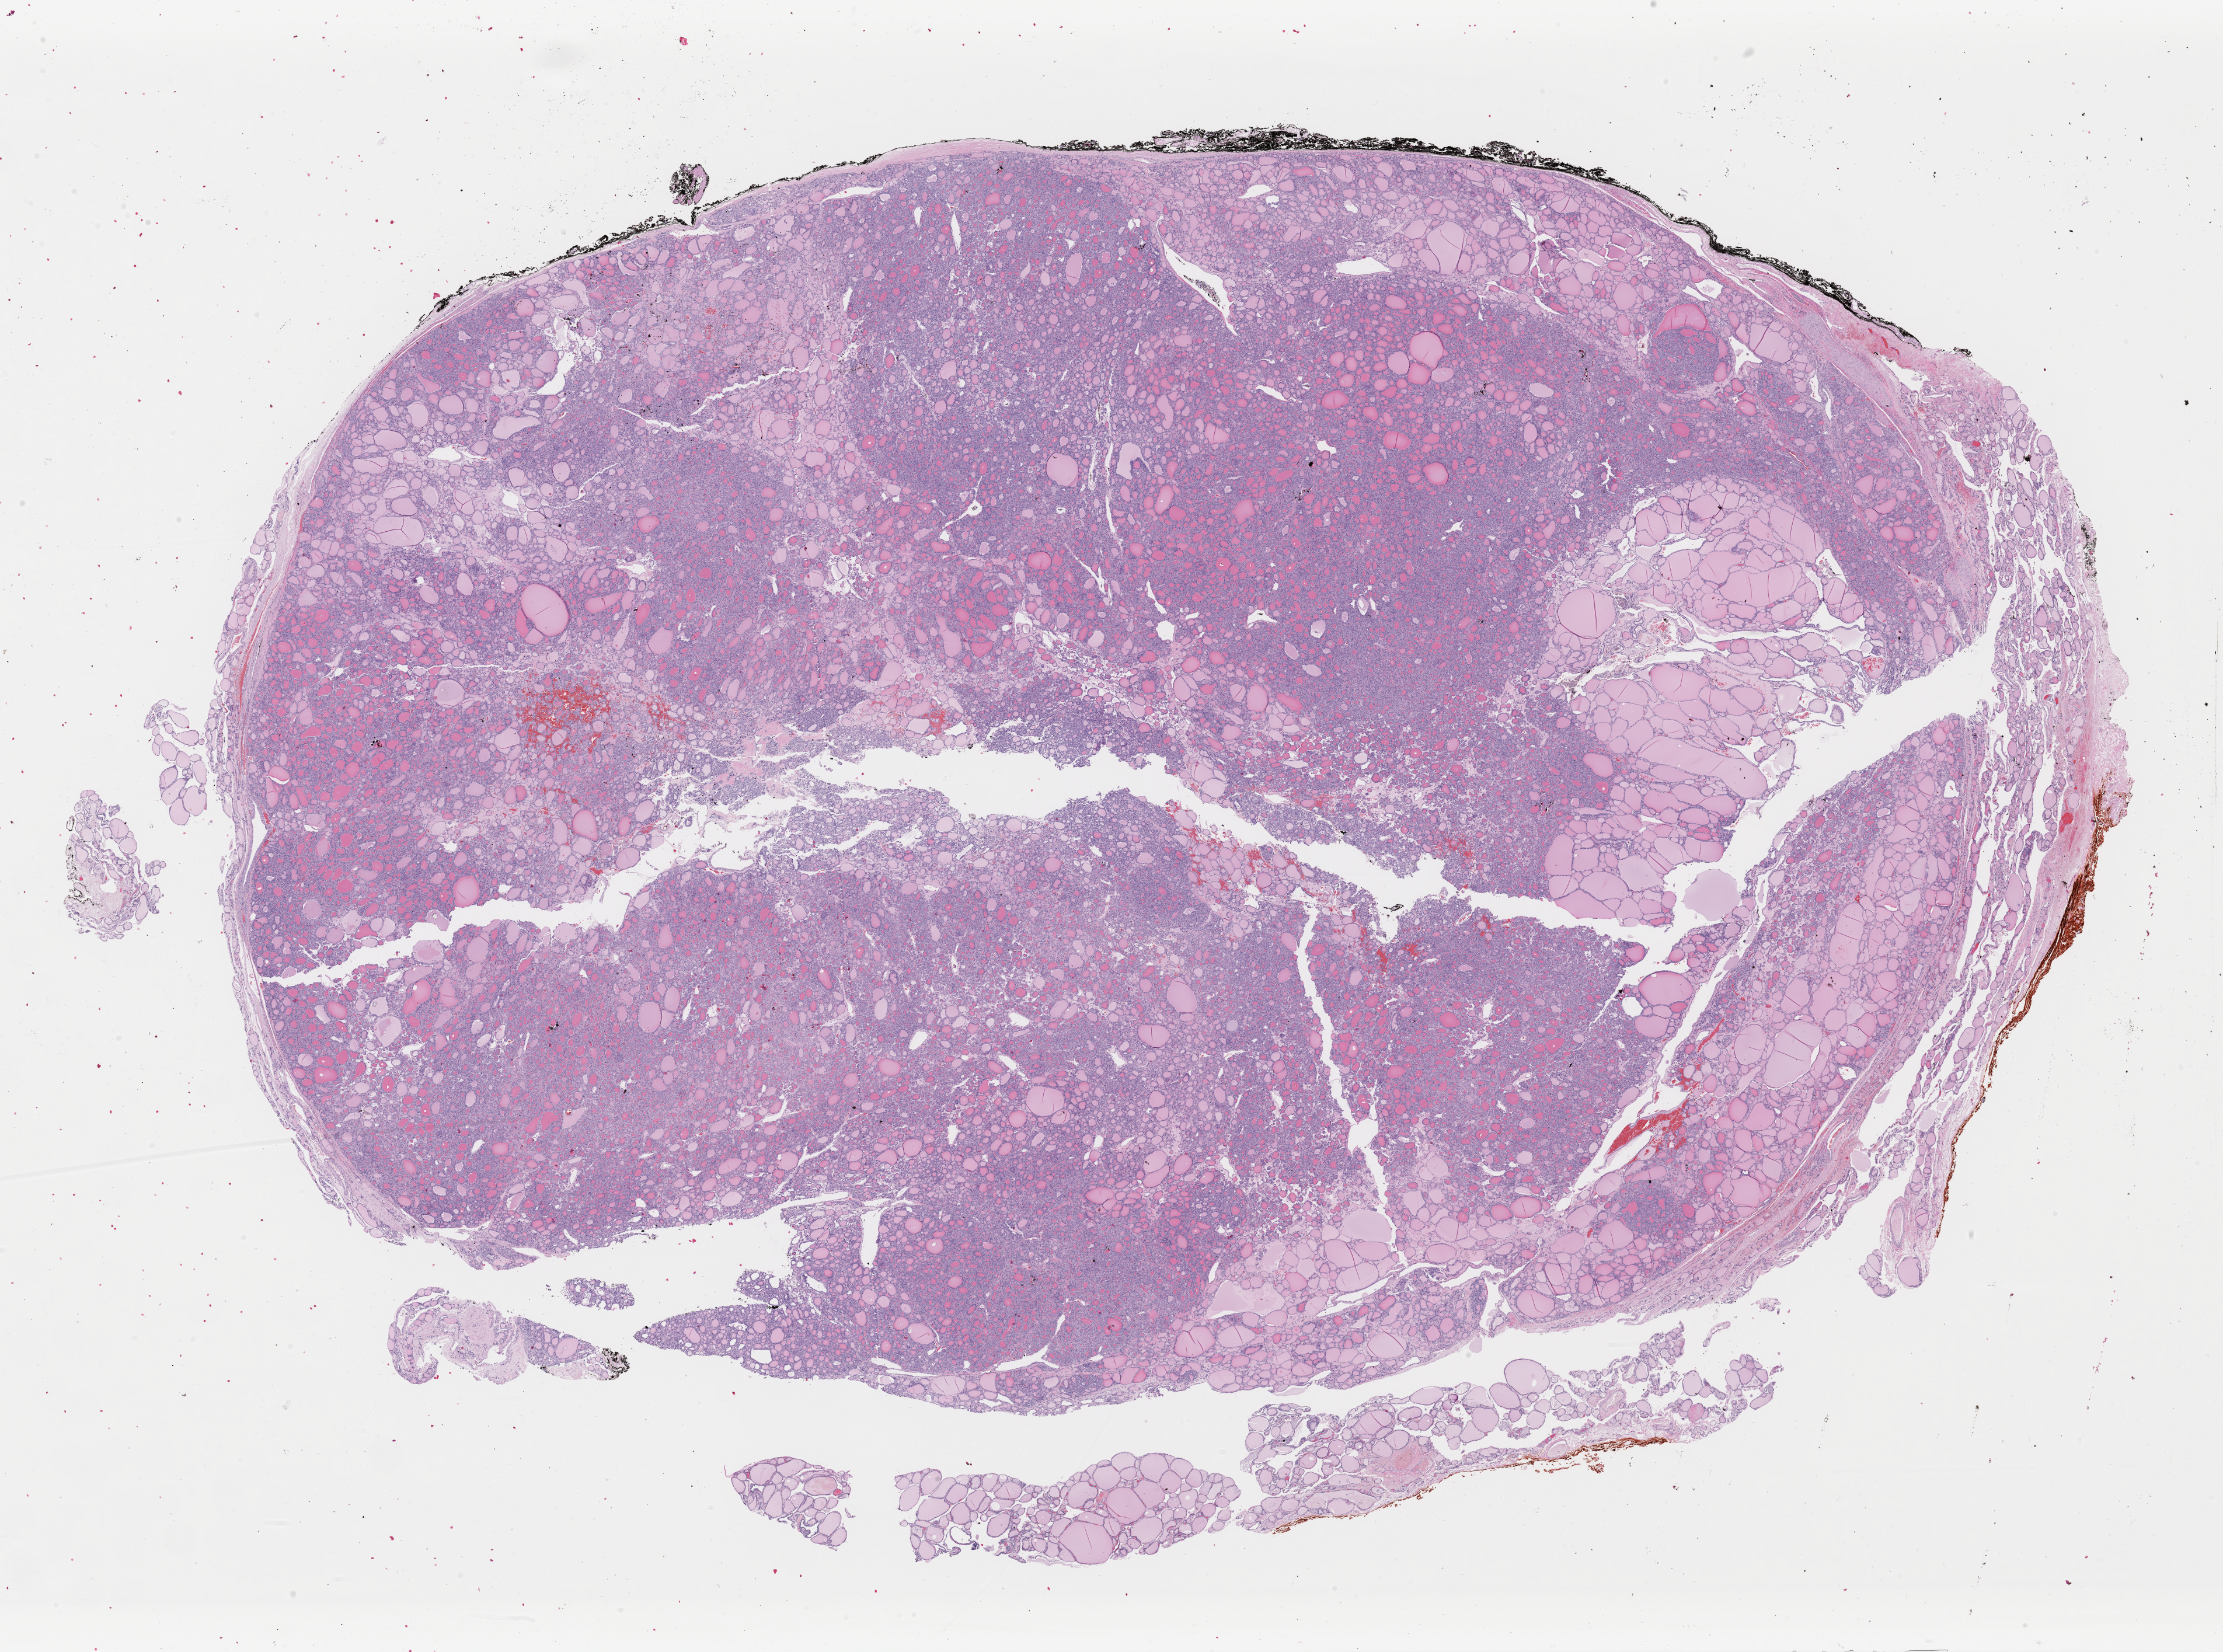
Digitized Hematoxylin and eosin (H&E) stained tissue section (whole slide) — shown as a low-resolution overview of the whole scanned area (about 30.1 x 22.4 mm); FFPE section; primary tumour sample from the thyroid. Patient: female, age at initial diagnosis 46 years.
Histologic diagnosis: Papillary carcinoma, follicular variant (thyroid gland). AJCC pathologic stage: III (6th edition).